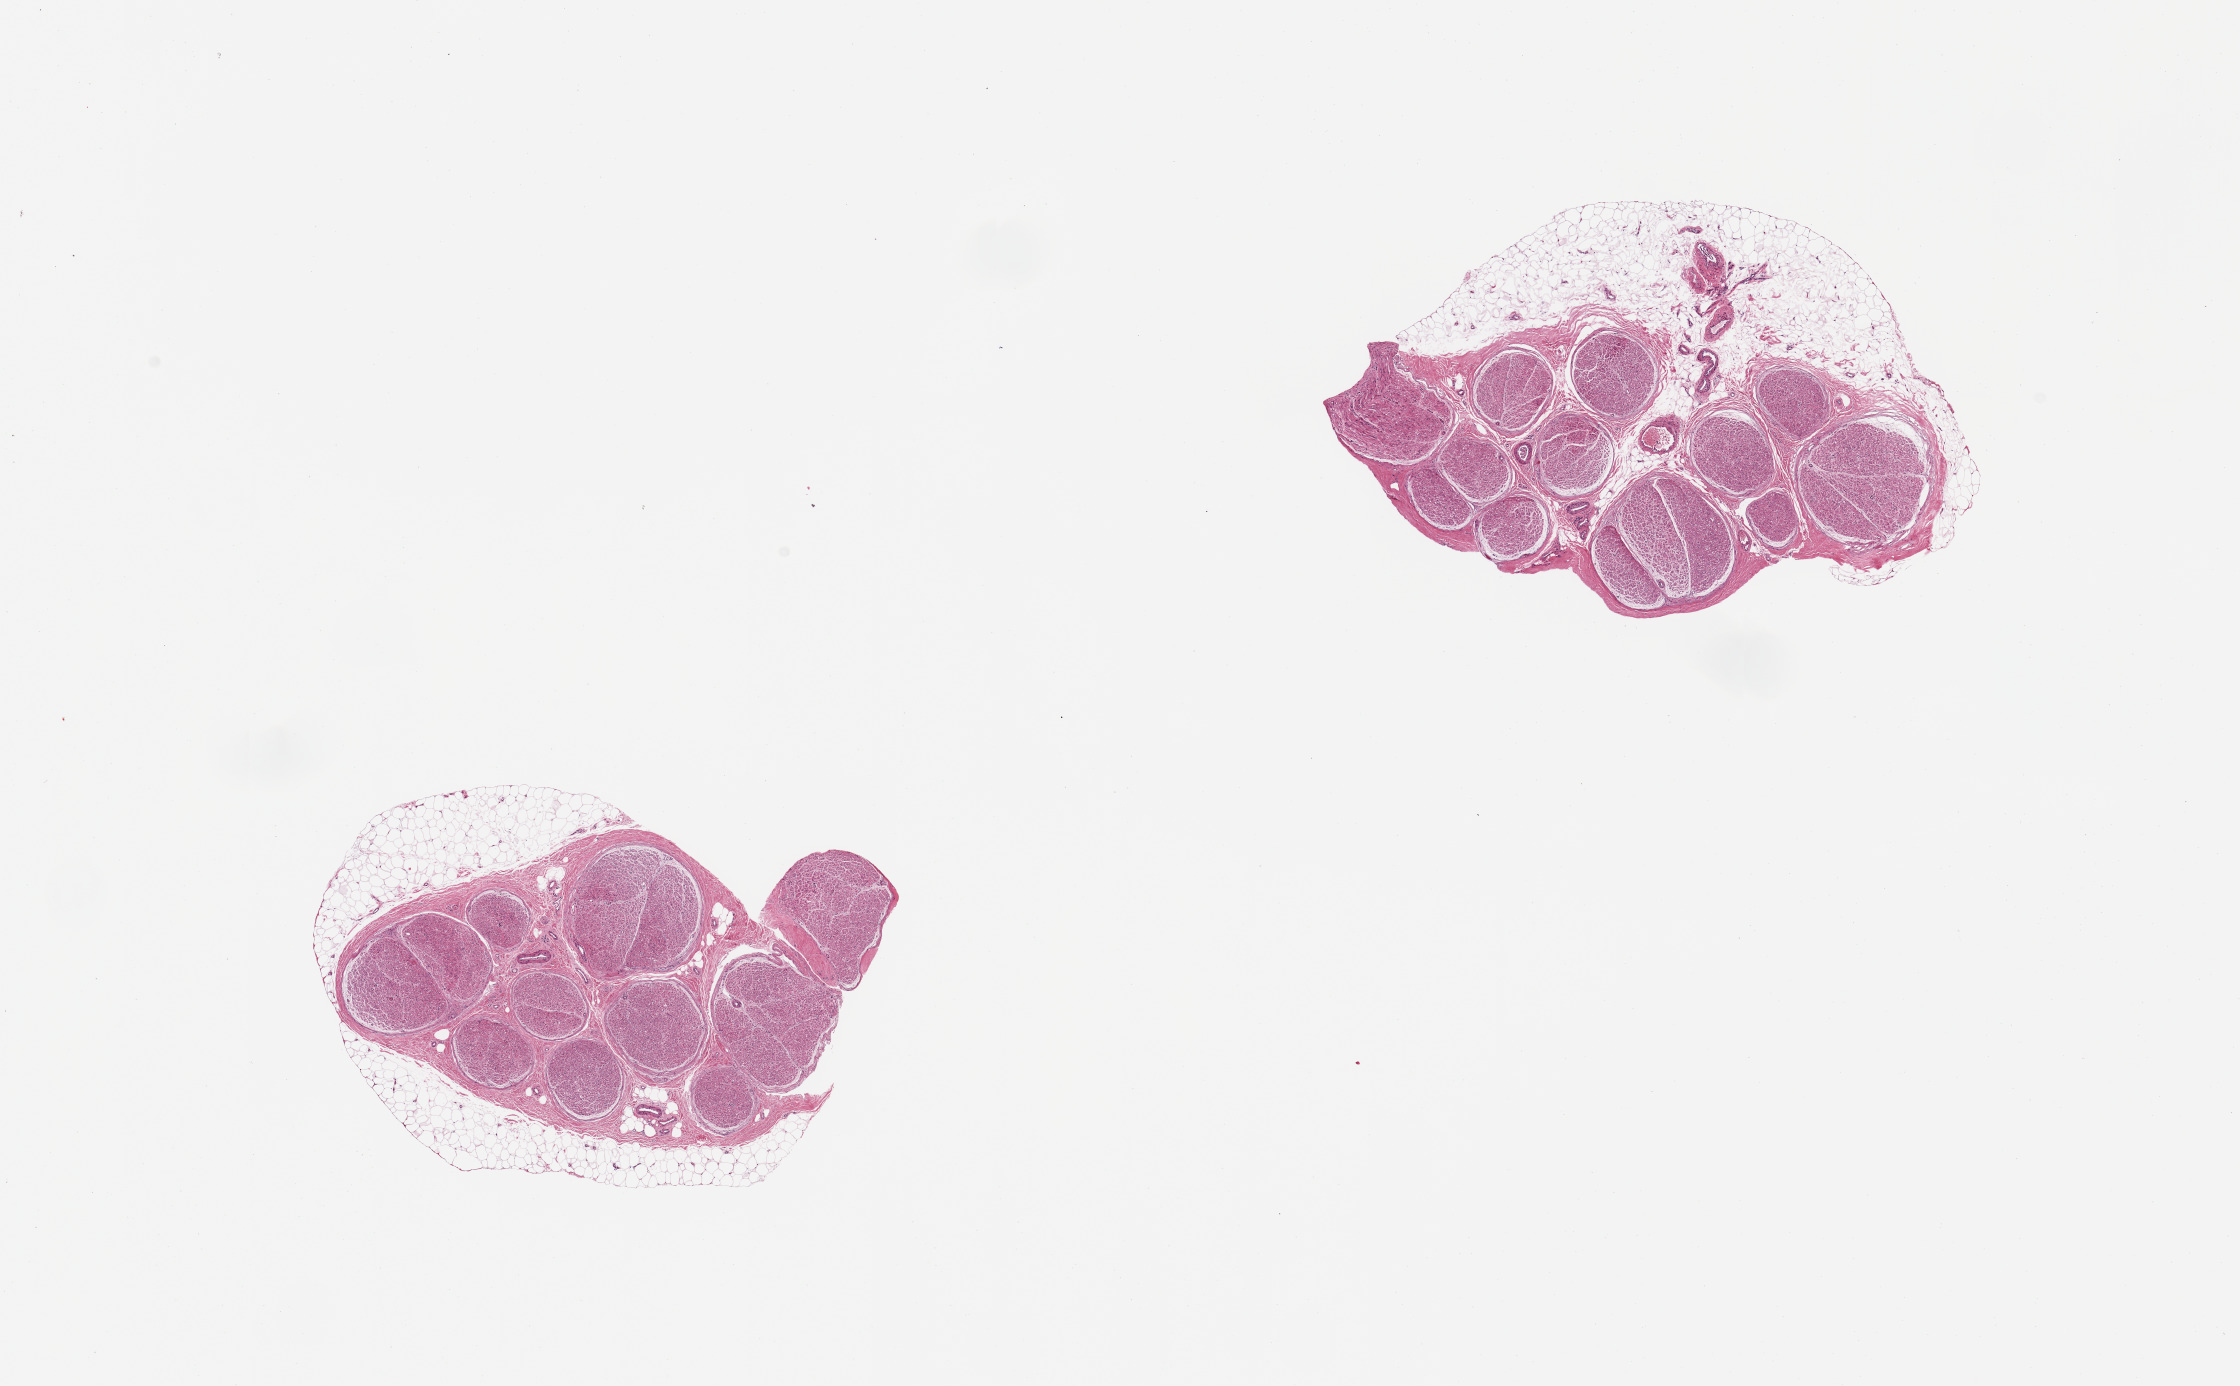
Whole-slide image, hematoxylin and eosin (H&E) stain, low-resolution overview of the scanned area, about 17.7 x 11.0 mm (slide scanned at 20x), PAXgene-fixed paraffin-embedded (PFPE) section, sampled site (target tissue): tibial nerve, donor tissue sample. Donor sex: male.
Pathologist's review note for this sample: 2 pieces; 20 & 30% external untrimmed fat.